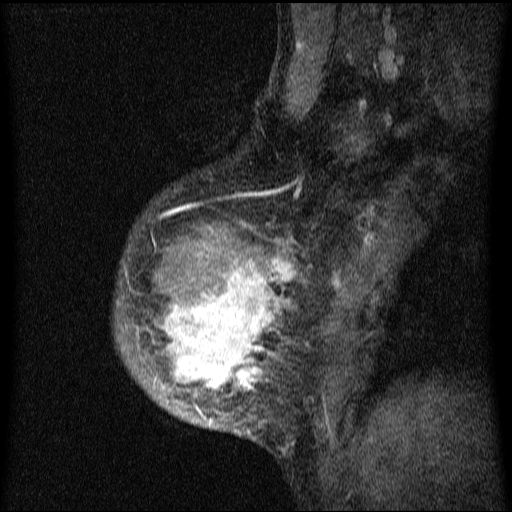
Breast MRI (dynamic contrast-enhanced), one sagittal slice. Position 51 of 64 along the scan axis. Dynamic contrast-enhanced series, image 2 of 4 at this slice position (ordered by acquisition). 1.5 T. TE 4.2 ms, TR 9.1 ms. 2 mm slice thickness. 512 × 512 image matrix, field of view 180 × 180 mm. Female patient, age 33 years.
Outlined on this slice (semi-automatically segmented with operator editing):
- analysis volume of interest (the breast-tissue region the enhancement analysis was run in; not a lesion): box from (x=115, y=164) to (x=335, y=457) px
- tumour enhancement mask (voxels above the 70 % enhancement threshold inside the analysis volume of interest): (x=131, y=193)–(x=299, y=434)